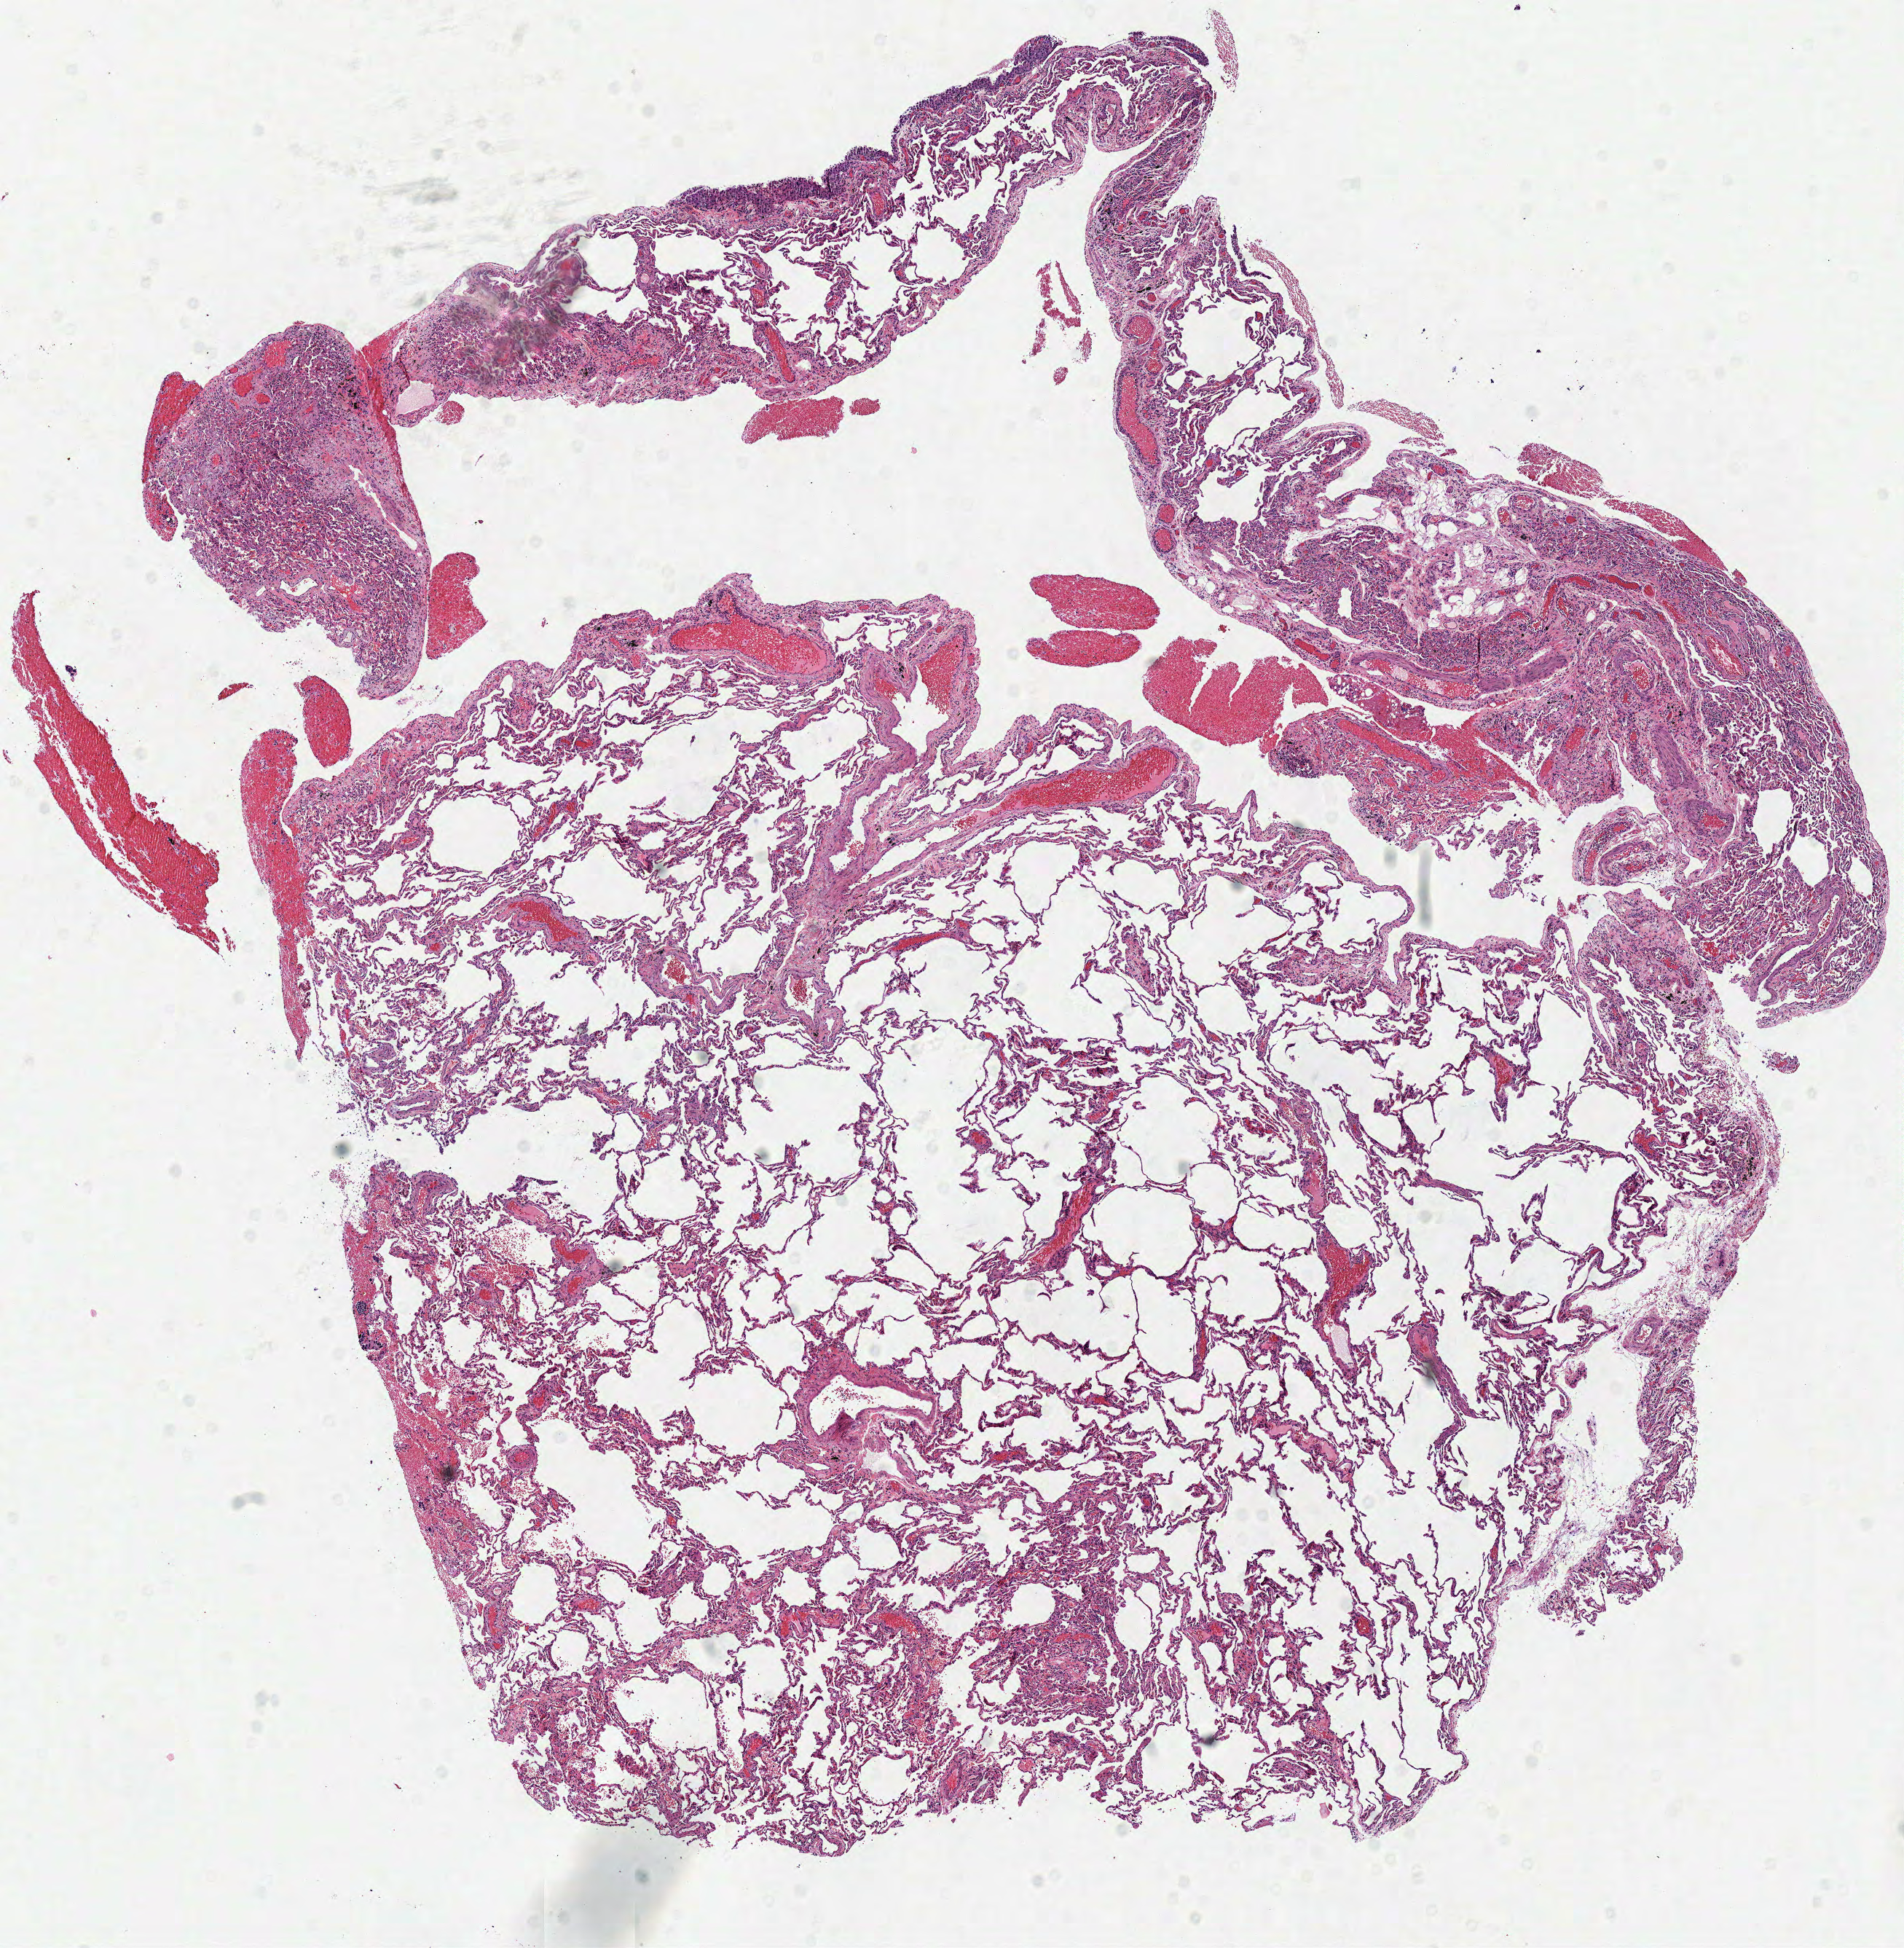
Digitized H&E-stained tissue section (whole slide), low-resolution overview of the scanned area, about 10.3 x 10.5 mm (from a 40x scan); frozen section from the top of the tissue portion; solid tissue normal (non-tumour tissue) sample from the lung. Female patient; age at initial diagnosis 56 years.
- this section: solid tissue normal (non-tumour) sample from the same patient
- patient diagnosis: Adenocarcinoma, NOS (lower lobe, lung)